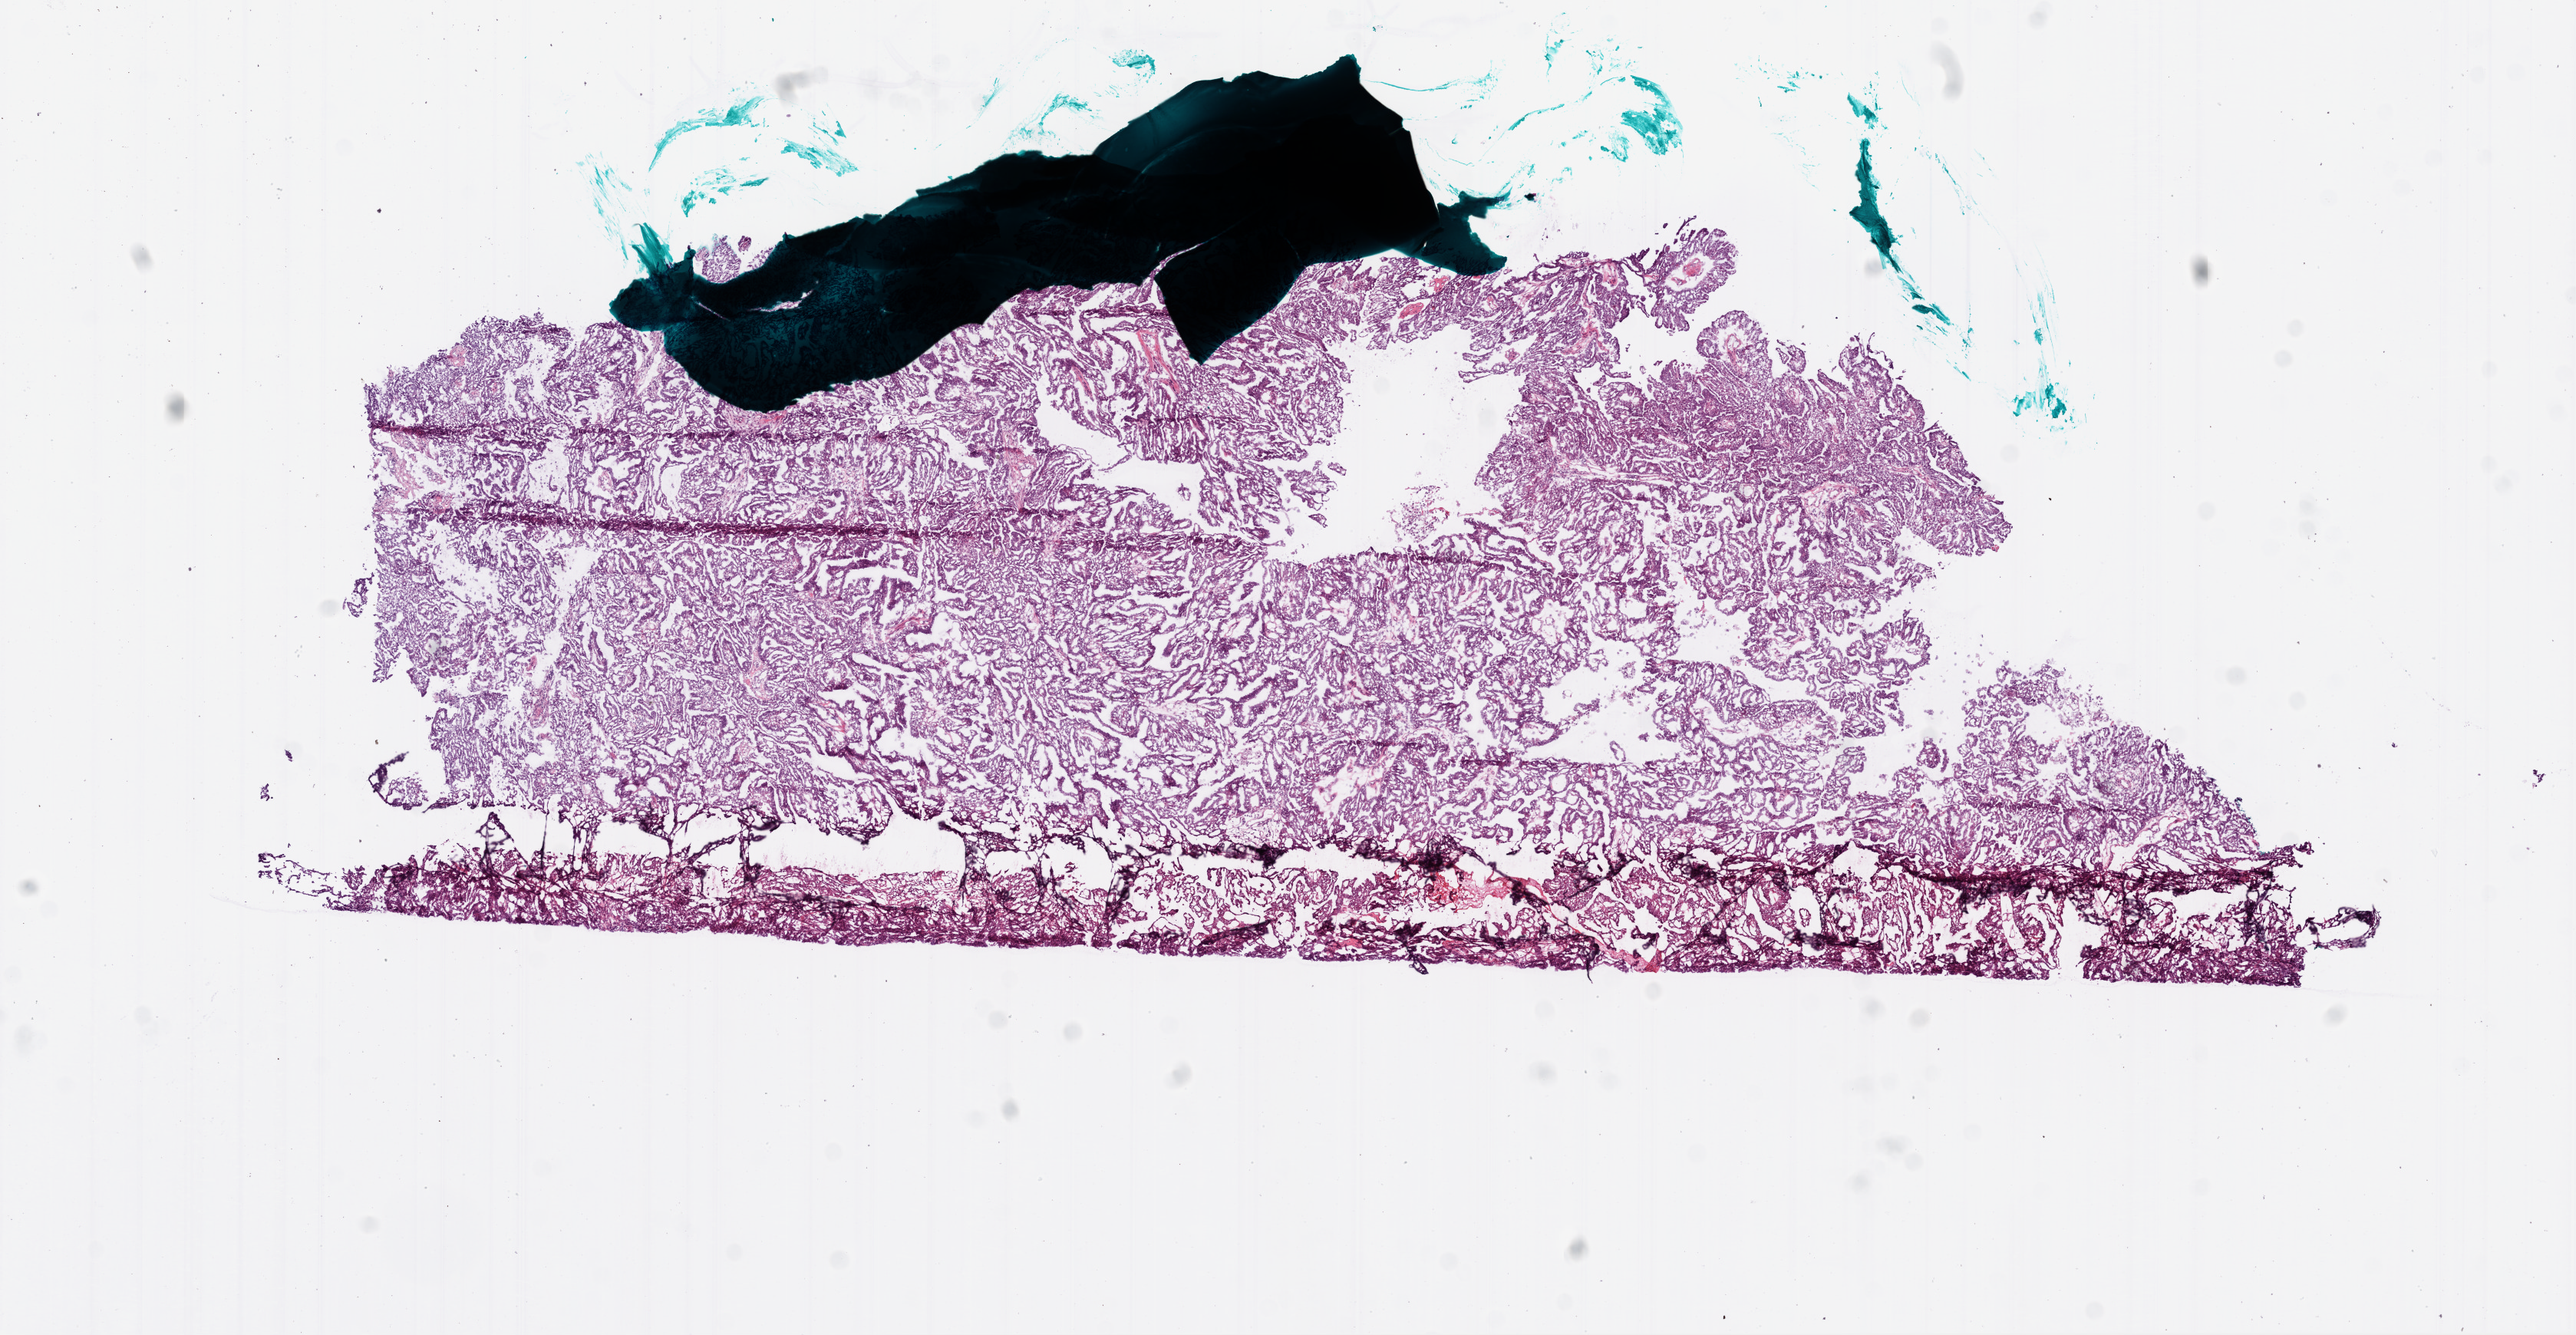
H&E whole-slide image, a low-resolution overview of the entire scanned area, about 13.5 x 7.0 mm (acquisition: 20x scan), frozen section from the bottom of the tissue portion, sample: primary tumour, ovary. Female patient; age at initial diagnosis 48 years. Histologic grade: G3 (poorly differentiated). Composition of this section per pathologist review: tumour cells 93%, tumour nuclei 94%, normal cells 5%, stromal cells 1%, necrosis 1%.
Diagnosis: Serous cystadenocarcinoma, NOS. FIGO stage: IIIC.